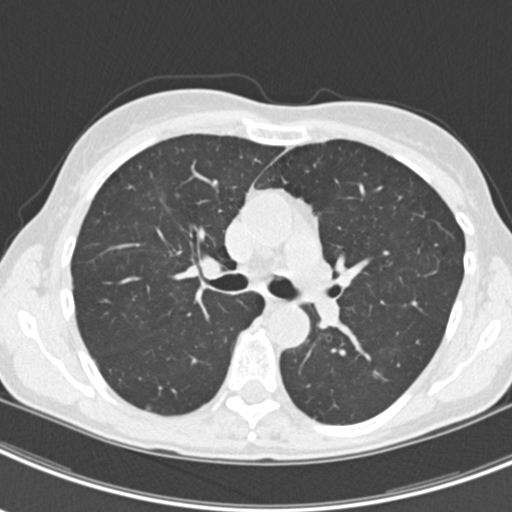
Low-dose screening chest CT, axial slice. Second screening round (one year after baseline). Lung window (W 1500 / L -600 HU). 2 mm slice thickness. 120 kVp. Slice 75 of 219 in the series. 512 × 512 image matrix. Female, age 63 years at enrolment. Current smoker at enrolment.
Expert reader's lesion annotation, box from (x=364, y=353) to (x=408, y=392) px. The screening reader recorded 9 non-calcified nodules or masses ≥4 mm on this exam (left upper lobe, right upper lobe, left upper lobe, left lower lobe, right middle lobe, left lower lobe, left lower lobe, right lower lobe, right lower lobe); which of them this box marks is not recorded. Lung cancer was diagnosed 408 days after this screen: bronchiolo-alveolar adenocarcinoma, NOS, right upper lobe, right middle lobe, right lower lobe, left upper lobe, left lower lobe, moderately differentiated (G2), stage IV (AJCC 6th edition).